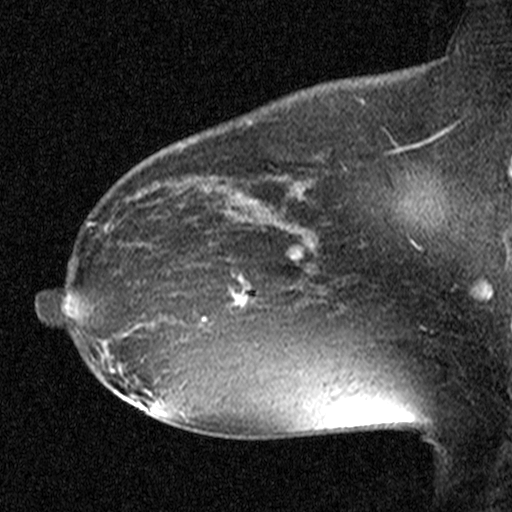
Breast MRI (dynamic contrast-enhanced), one sagittal slice; slice 30 of 44 in the series (ordered by position); dynamic contrast-enhanced study with each time point stored as its own series, time point 2 of 3 at this slice position (early post-contrast, ordered by acquisition time); 1.5 T; TE 4.5 ms, TR 11 ms; 512 × 512 image matrix, field of view 200 × 200 mm. Patient: female, 38 years. Case-level facts recorded for this patient, not image findings: setting: breast cancer imaged before/during neoadjuvant chemotherapy; receptor status: HR-positive, HER2-negative.
Structures marked on this image (semi-automatically segmented with operator editing):
- analysis volume of interest (the breast-tissue region the enhancement analysis was run in; not a lesion): bounding box (x1, y1, x2, y2) in pixels: (182, 232, 291, 349)
- tumour enhancement mask (voxels above the 90 % enhancement threshold inside the analysis volume of interest): (203, 236, 245, 320)